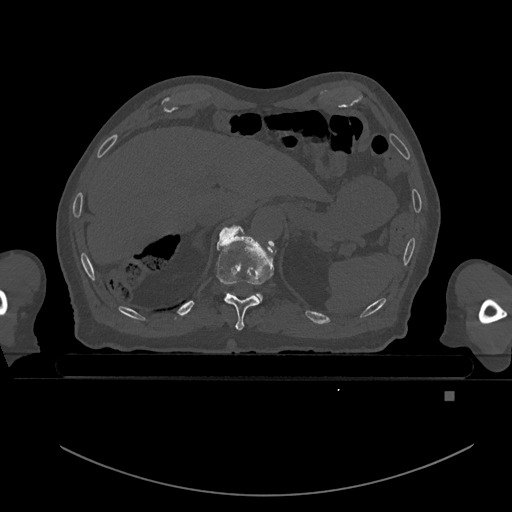
CT including the spine, one axial slice. Position 75 of 969 along the scan axis. Bone window (W 1800 / L 400 HU). 0.5 mm slice thickness. 512 × 512 image matrix, field of view 456 × 456 mm. Male patient, age 82 years. From the clinical record (not read from this slice): primary cancer: prostate.
Outlined on this slice (semi-automatically segmented with operator editing):
- T10 vertebra: box from (x=216, y=225) to (x=275, y=331) px
- T11 vertebra: (x=254, y=294)–(x=263, y=302)